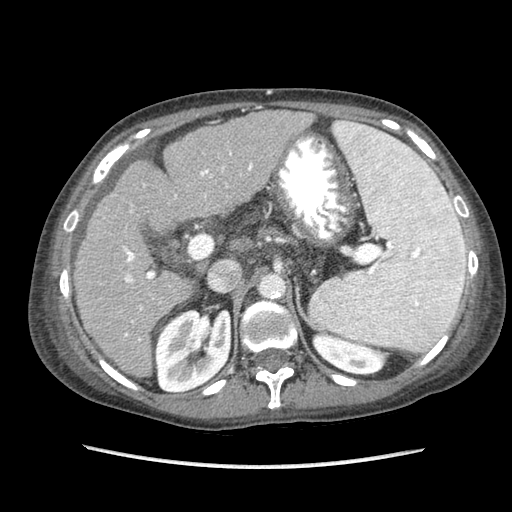
Contrast-enhanced abdominal CT (liver protocol), one axial slice. Slice 48 of 87 in the series (ordered by position). Soft-tissue window (W 400 / L 40 HU). 2.5 mm slice thickness. 512 × 512 image matrix, field of view 340 × 340 mm. From the clinical record (not read from this slice): diagnosis: hepatocellular carcinoma (patient treated with transarterial chemoembolisation; whether this scan precedes or follows treatment is not stated here); TNM stage (as recorded): Stage-IIIB; Child-Pugh class: A.
Outlined on this slice (semi-automatic segmentation, software-assisted and operator-edited):
- liver parenchyma outside the tumour (the mass and vessels are separate outlines, so this box may not span the whole liver): bounding box (x1, y1, x2, y2) in pixels: (74, 110, 314, 376)
- liver vessels: (124, 151, 253, 341)